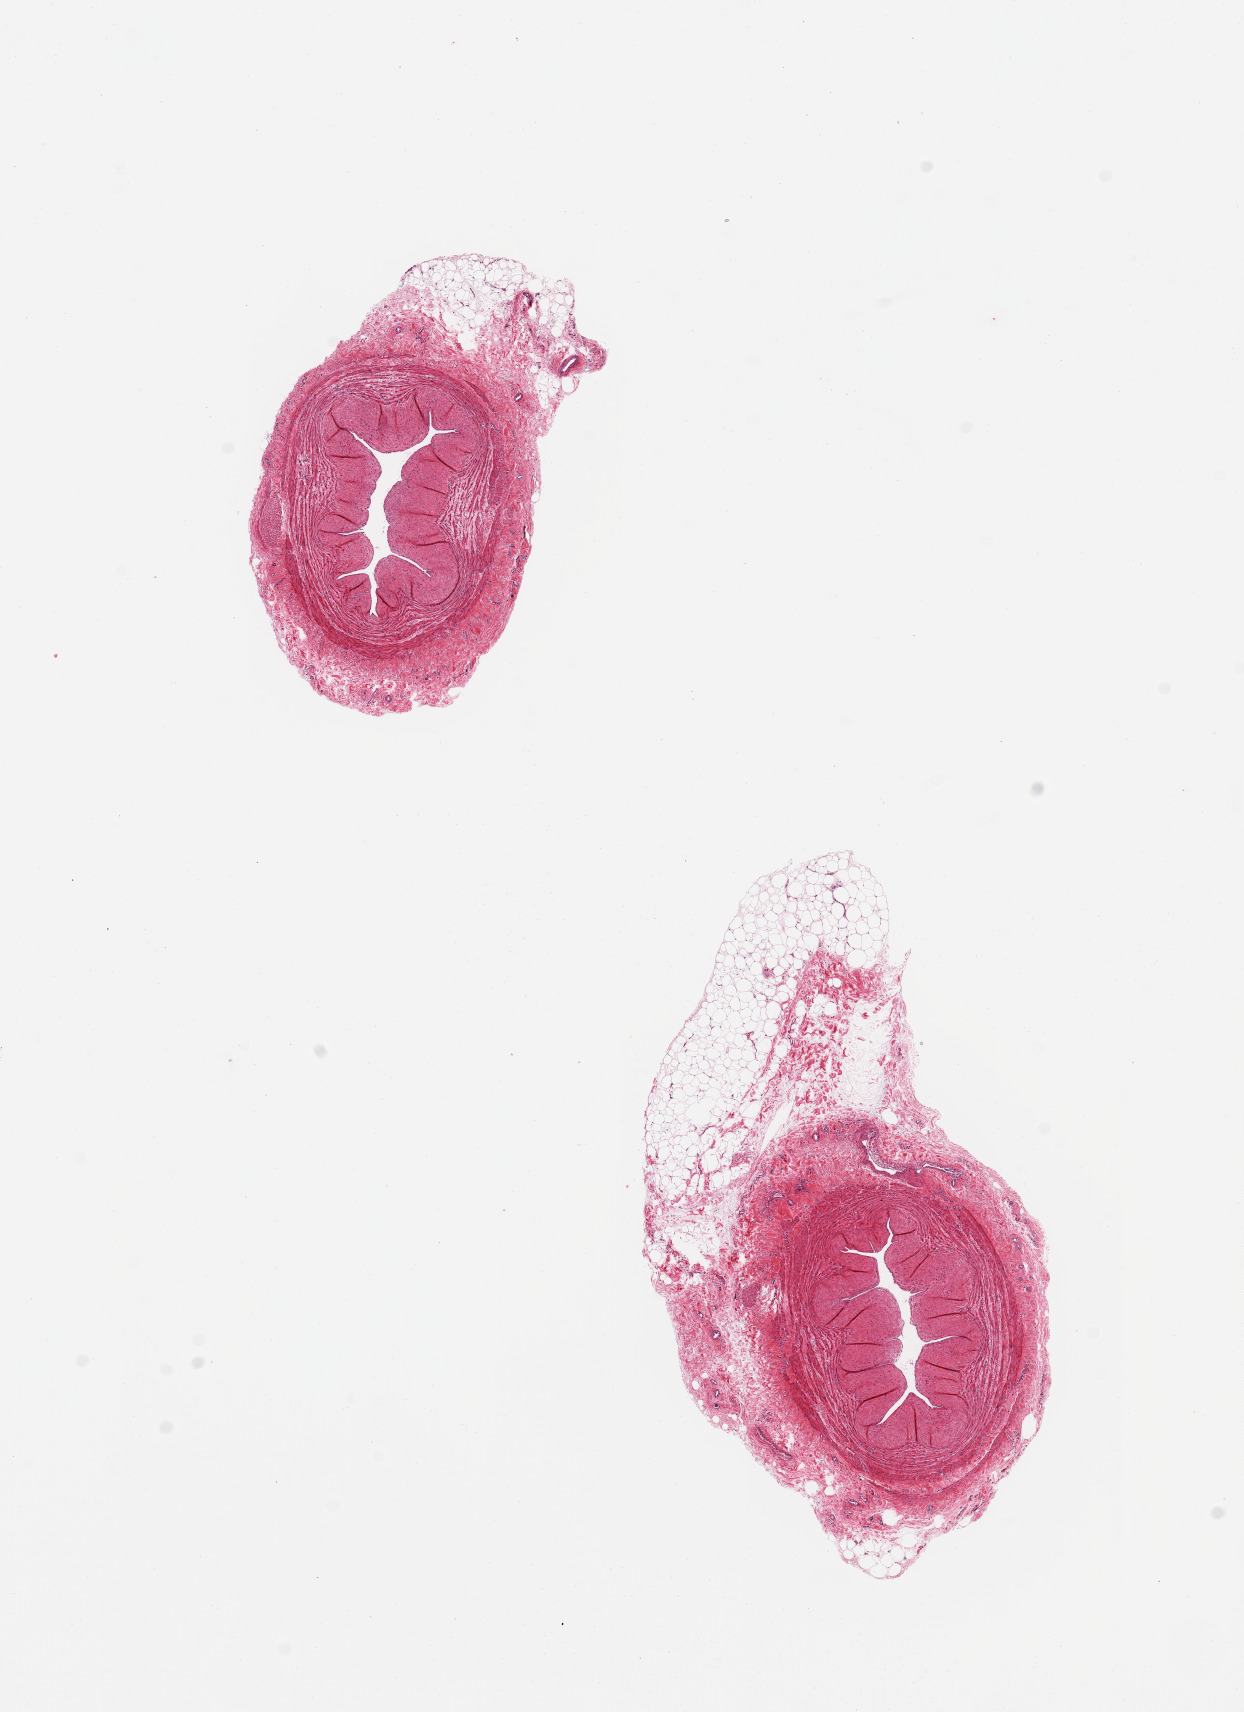
Digitized hematoxylin and eosin (H&E)-stained section, brightfield — low-resolution overview of the scanned area, about 9.8 x 13.5 mm (acquisition: 20x scan). PAXgene-fixed, paraffin-embedded tissue. Sampled site (target tissue): tibial artery. Tissue donor sample. Donor sex: male.
Reviewer comment on this tissue sample: 2 pieces; no plaques; external fat up to 2mm thick.